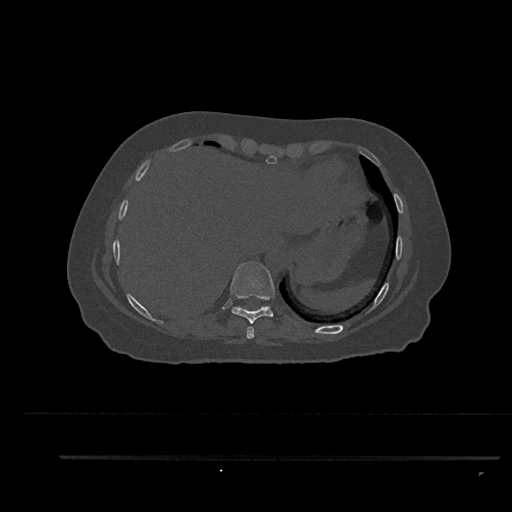
CT including the spine, one axial slice; position 408 of 797 along the scan axis; bone window (W 1800 / L 400 HU); 0.5 mm slice thickness; 512 × 512 image matrix, field of view 408 × 408 mm. Female patient, age 44 years. Case-level facts recorded for this patient, not image findings: primary cancer: renal.
Annotated regions visible in this slice (semi-automatically segmented with operator editing):
- T8 vertebra: bounding box [x1, y1, x2, y2] px = [246, 326, 255, 339]
- T9 vertebra: [230, 261, 275, 324]